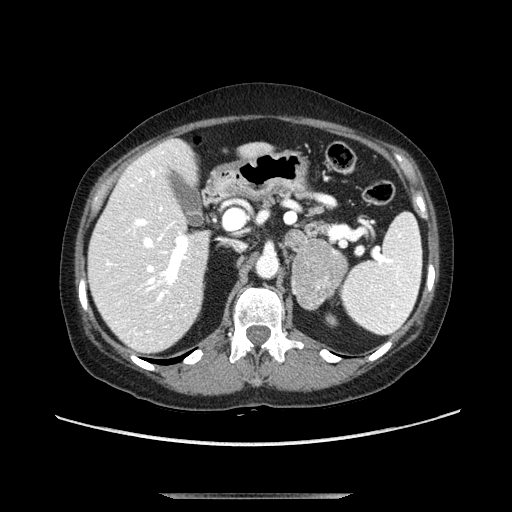
Contrast-enhanced abdominal CT, one axial slice. Slice 65 of 107 in the series (ordered by position). Soft-tissue window (W 400 / L 40 HU). 512 × 512 image matrix, field of view 380 × 380 mm. Female patient. From the clinical record (not read from this slice): diagnosis: adrenocortical carcinoma; tumour side: left adrenal; tumour size at pathology: 7.5 cm; Ki-67 index: 9 %; stage (as recorded): 3.
Outlined on this slice (semi-automatic segmentation, software-assisted and operator-edited):
- mass: box from (x=290, y=239) to (x=348, y=310) px